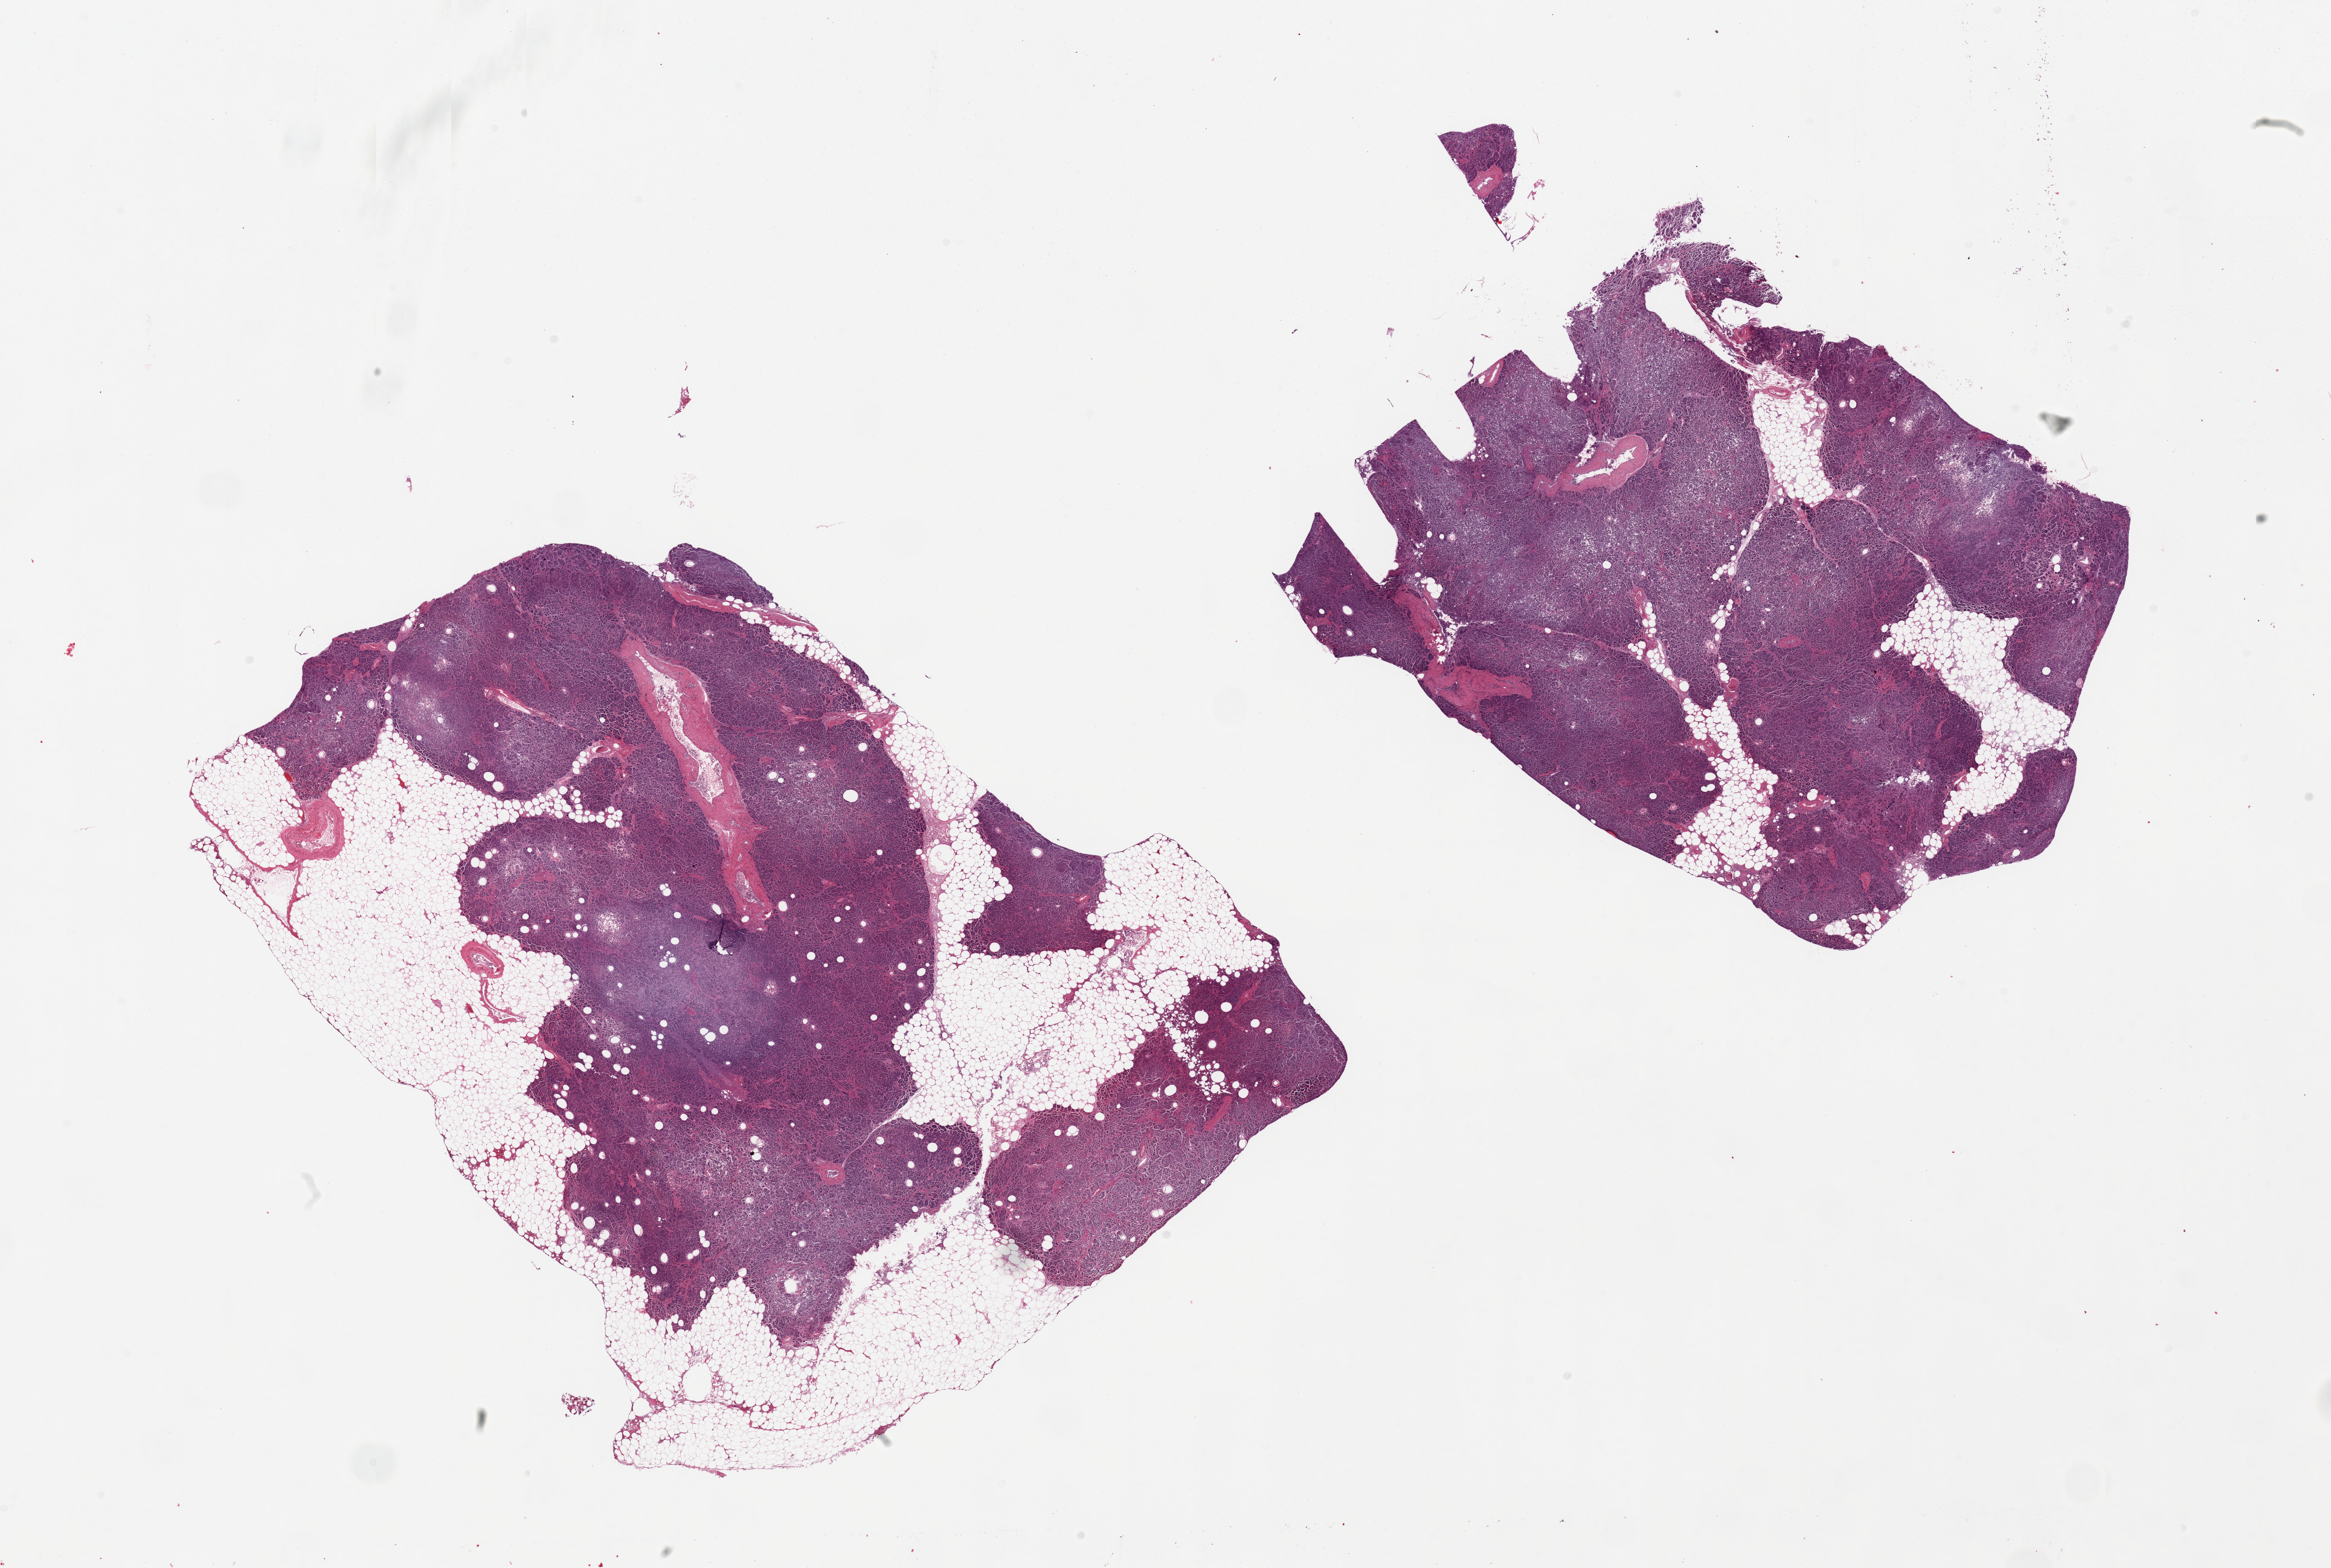
Digitized hematoxylin and eosin (H&E)-stained section, brightfield — whole scanned area (about 30.5 x 20.5 mm) shown as a low-resolution overview. PAXgene-fixed, paraffin-embedded tissue. Sampled site (target tissue): pancreas. Tissue donor sample. Male donor.
- reviewer comment on this tissue sample: 2 pieces, one piece is 50% fat, 2nd is 10% fat